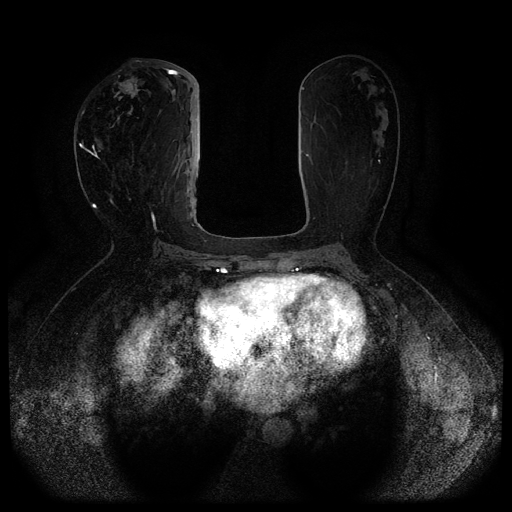
Breast MRI (dynamic contrast-enhanced, multi-phase), one axial slice. Position 43 of 116 along the scan axis. Dynamic contrast-enhanced series, time point 2 of 5 at this slice position (early post-contrast). 1.5 T. TE 2.6 ms, TR 5.3 ms. 2 mm slice thickness. 512 × 512 image matrix, field of view 350 × 350 mm. Female patient, age 51 years.
Annotated regions visible in this slice (semi-automatic segmentation, software-assisted and operator-edited):
- breast lesion (labelled 'tumour' in the annotation; benign lesions carry a separate 'benign' label): bounding box (x1, y1, x2, y2) in pixels: (114, 75, 146, 109)